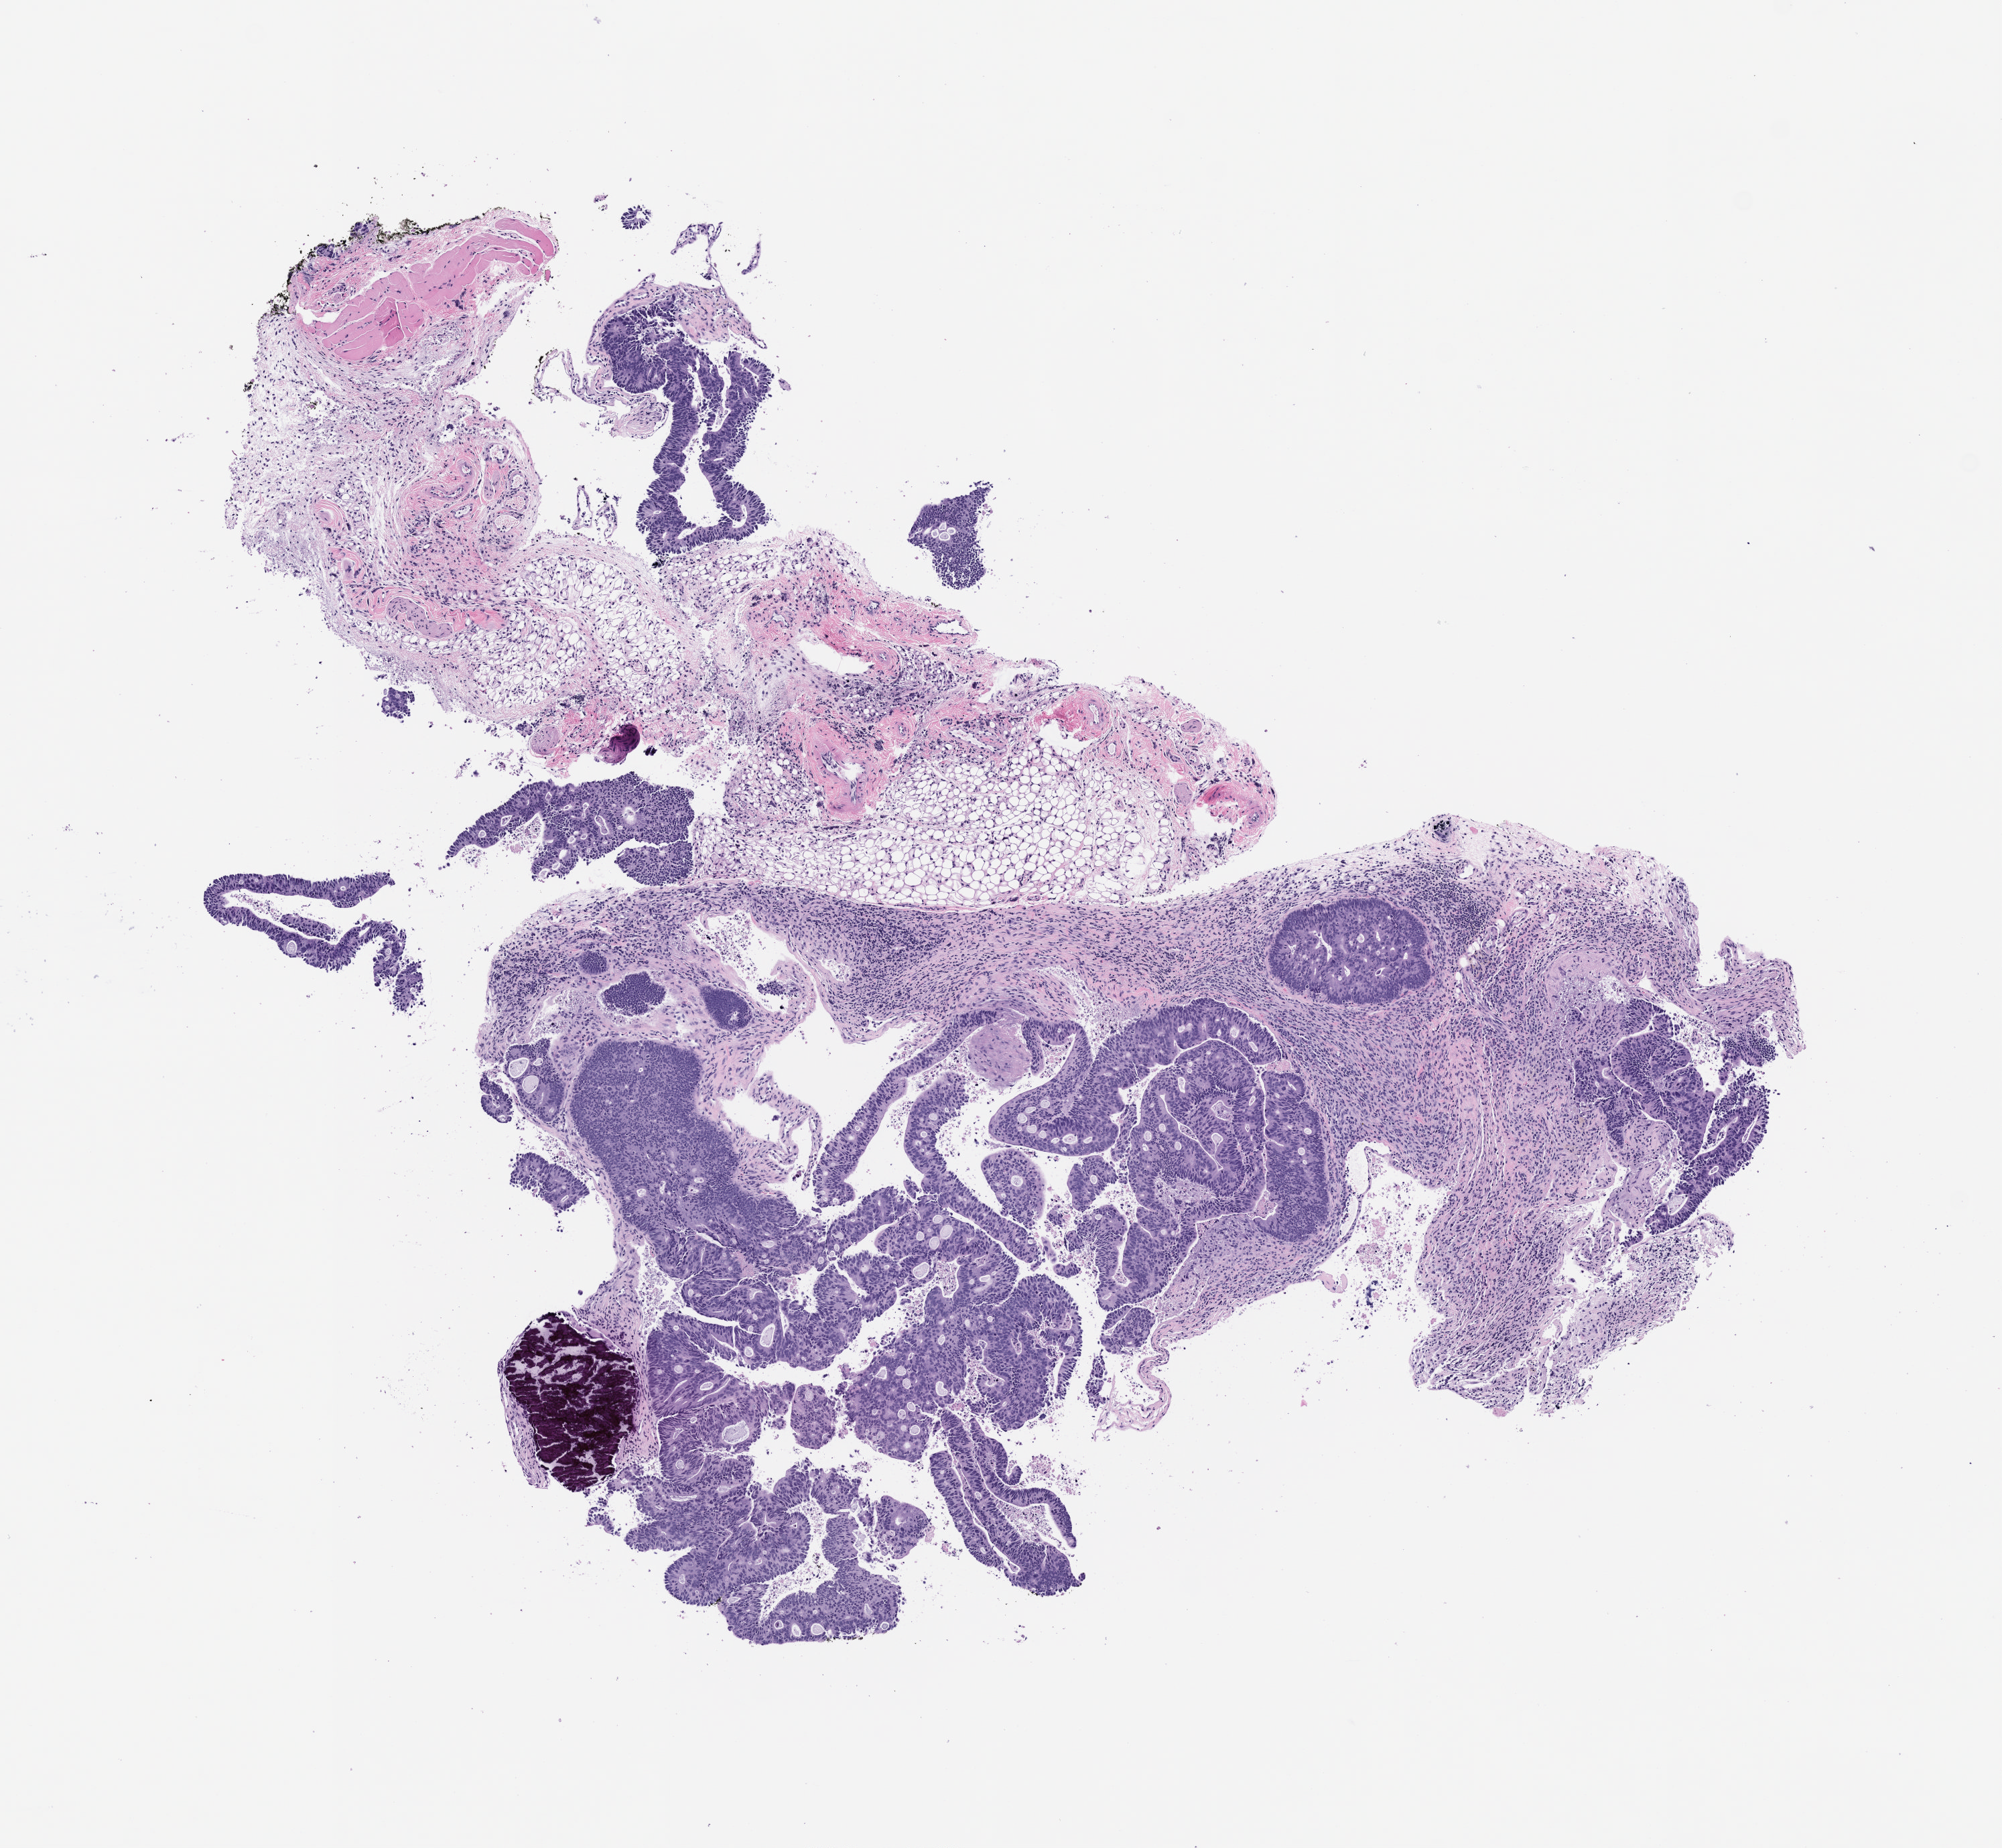
Haematoxylin and eosin whole-slide image of a patient-derived xenograft (PDX) tumor grown in a mouse, passage 1, low-resolution overview of the scanned area, about 6.0 x 5.5 mm. Formalin-fixed, paraffin-embedded (FFPE) tissue. Originating tumor site category: colon.
* originating patient diagnosis: Colon Adenocarcinoma